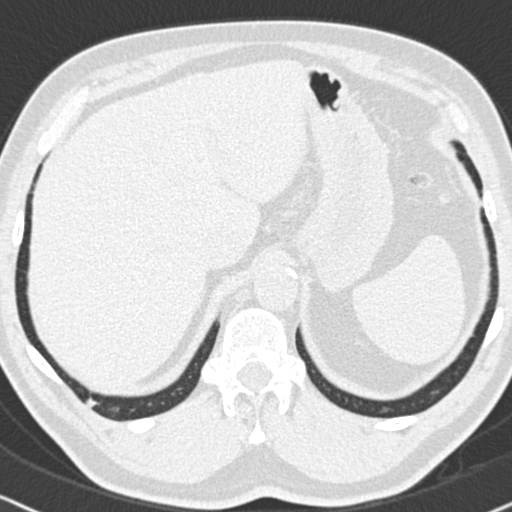
Axial slice from a low-dose chest CT screening exam, baseline screening round, lung window (W 1500 / L -600 HU), 2 mm slice thickness, slice 150 of 186 in the series, 512 × 512 image matrix, field of view 325 × 325 mm. Male participant, aged 63 years at enrolment. Former smoker at enrolment.
Lesion marked by an expert reader, box from (x=77, y=388) to (x=104, y=416) px. No non-calcified nodule or mass ≥4 mm was recorded by the screening reader at this exam. Later outcome: lung cancer diagnosed 626 days after this screen — adenocarcinoma, NOS, right lower lobe, moderately differentiated (G2), stage IIIB (AJCC 6th edition), 17 mm at pathology.